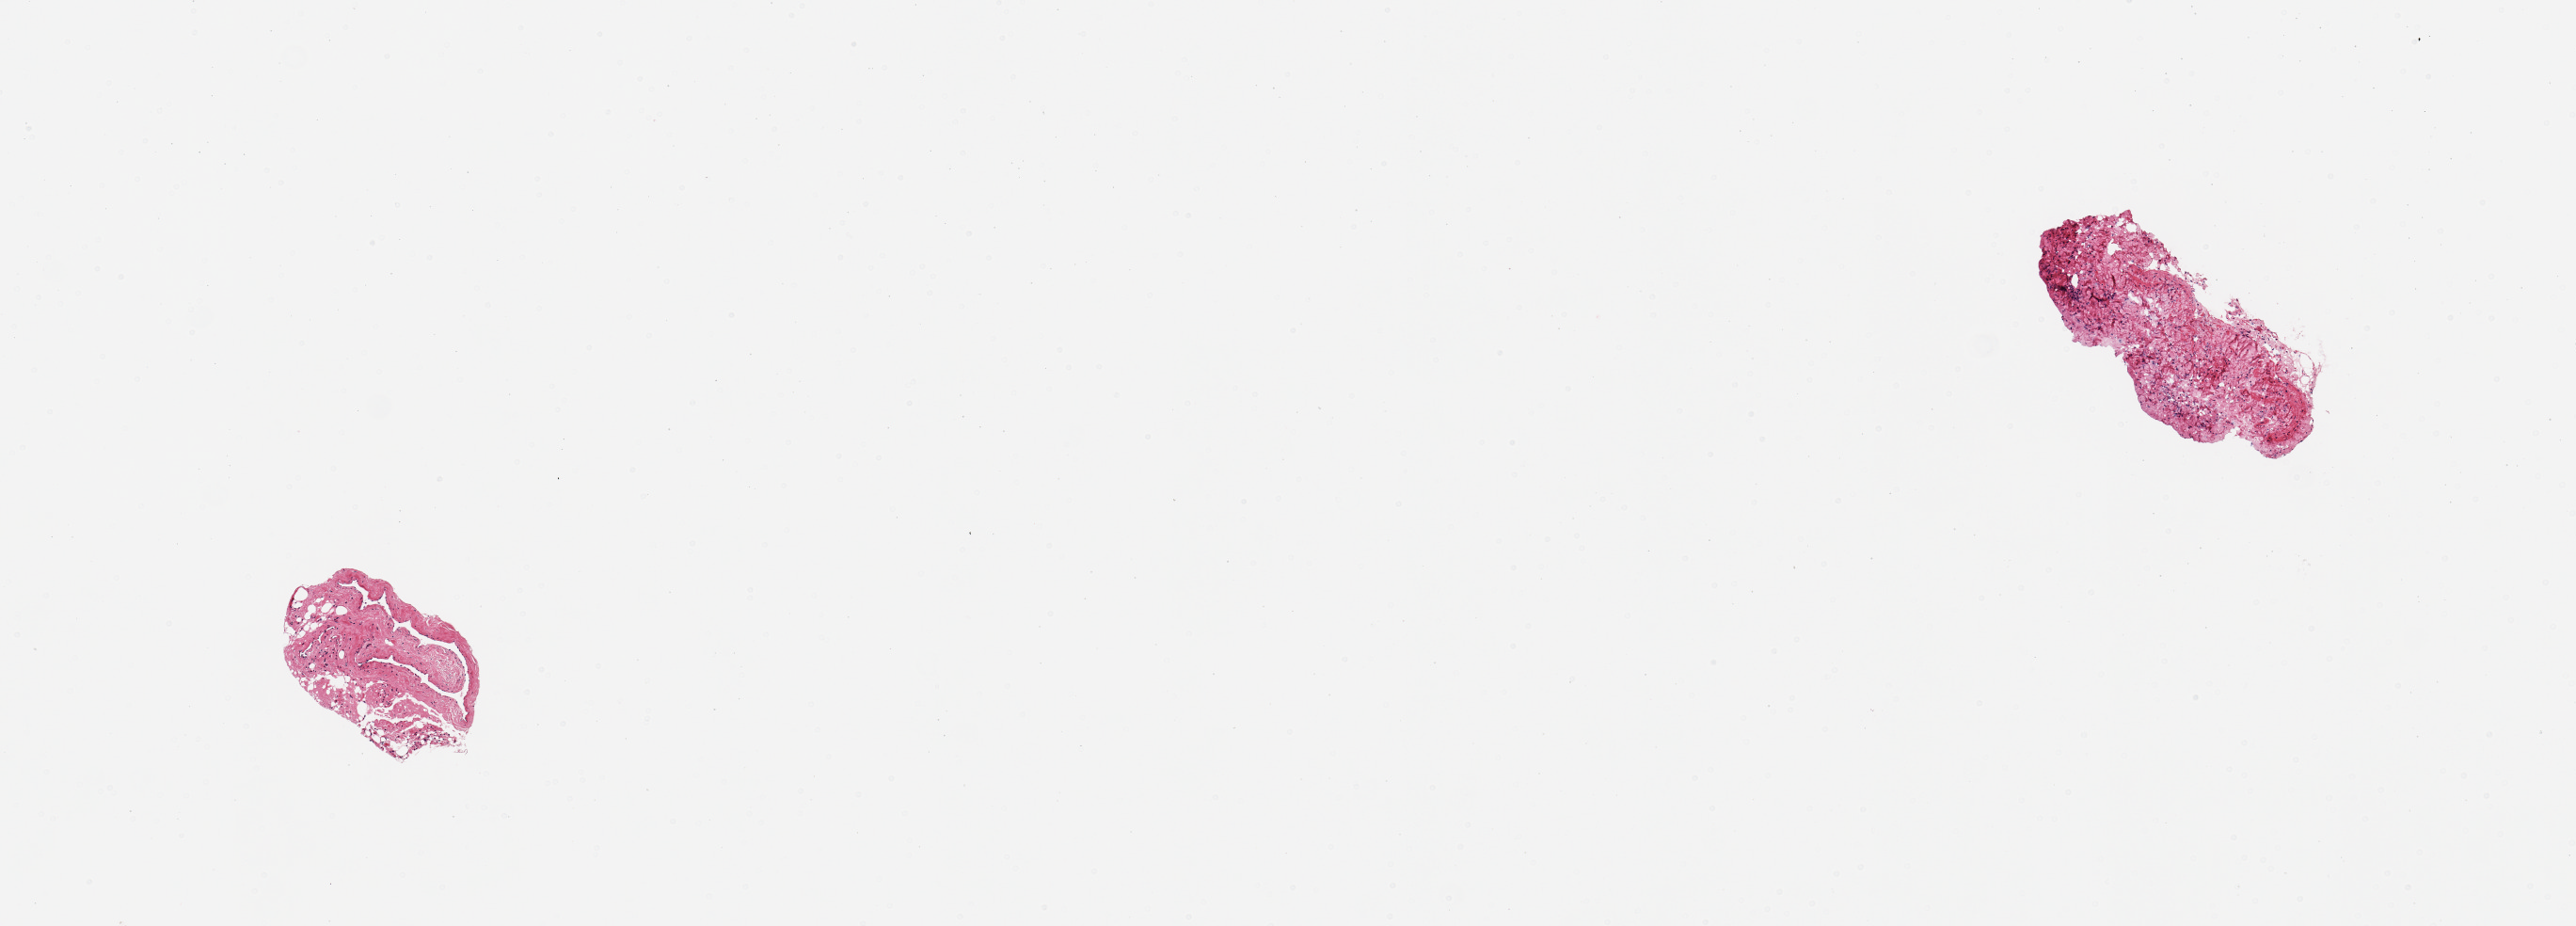
Whole-slide image, hematoxylin and eosin (H&E) stain — shown as a low-resolution overview of the whole scanned area (about 10.8 x 3.9 mm). PAXgene-fixed paraffin-embedded (PFPE) section. Sampled site (target tissue): coronary artery. Tissue donor sample. Male donor.
- pathologist's review note for this sample: 2 pieces; no coronary artery: 1 is vein, other is fatty tissue